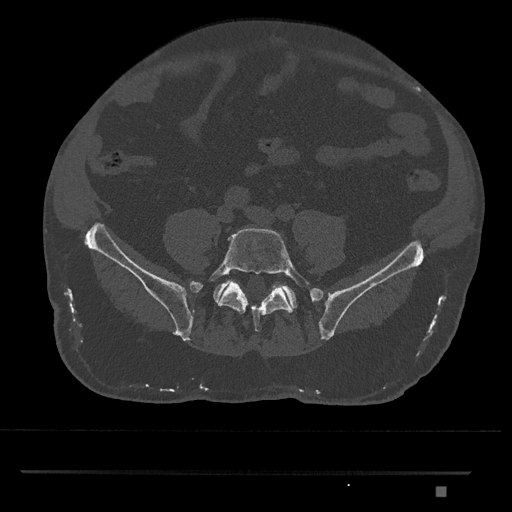
CT including the spine, one axial slice. Position 549 of 1134 along the scan axis. Reconstruction kernel Br40s/3. 120 kVp. Bone window (W 1800 / L 400 HU). 0.5 mm slice thickness. 512 × 512 image matrix, field of view 429 × 429 mm. Patient: male, 65 years. From the clinical record (not read from this slice): primary cancer: prostate.
Outlined on this slice (semi-automatically segmented with operator editing):
- L5 vertebra: bounding box [x1, y1, x2, y2] px = [209, 228, 311, 332]